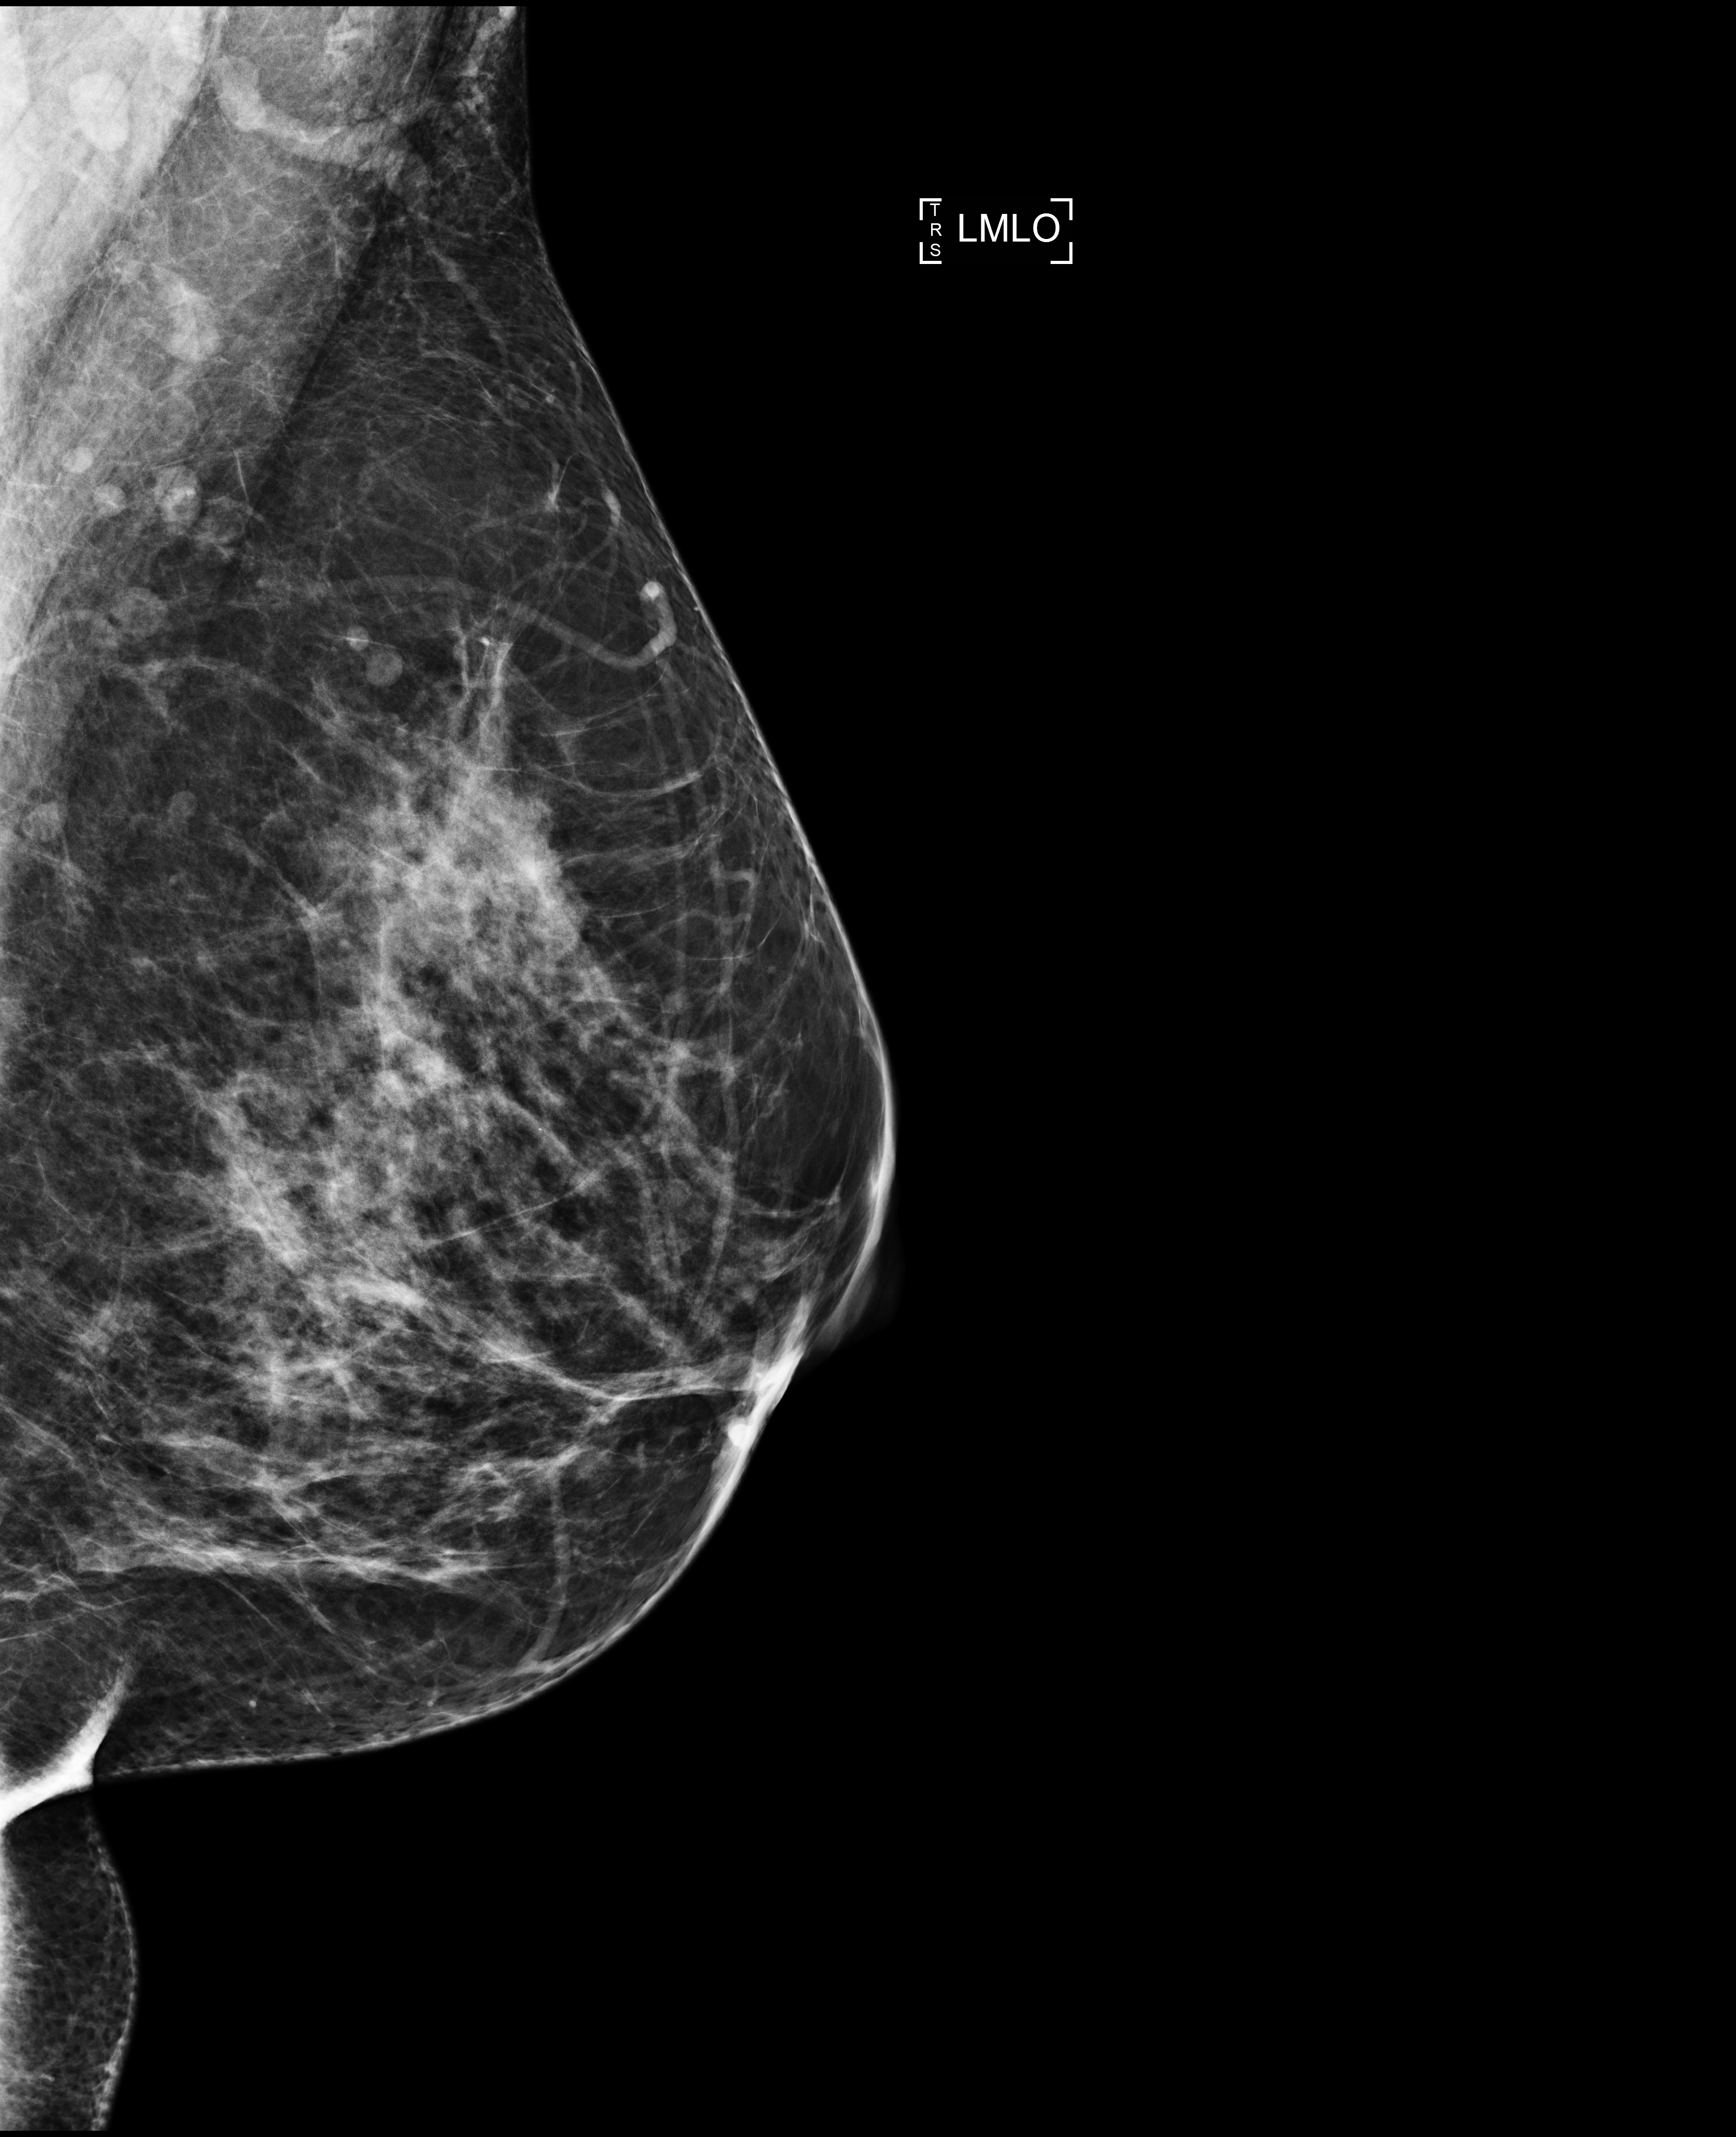
Full-field digital mammogram (FFDM), left breast, mediolateral oblique (MLO) view, annual screening mammography examination, compressed breast thickness 71 mm, system: Selenia Dimensions. Patient aged 44 years (female).
- BI-RADS breast density category at the screening exam (both breasts, scale 1–4): 3
- final BI-RADS category for the screening round (tomosynthesis exam, both breasts): category 2
- recall: no recall after this screen